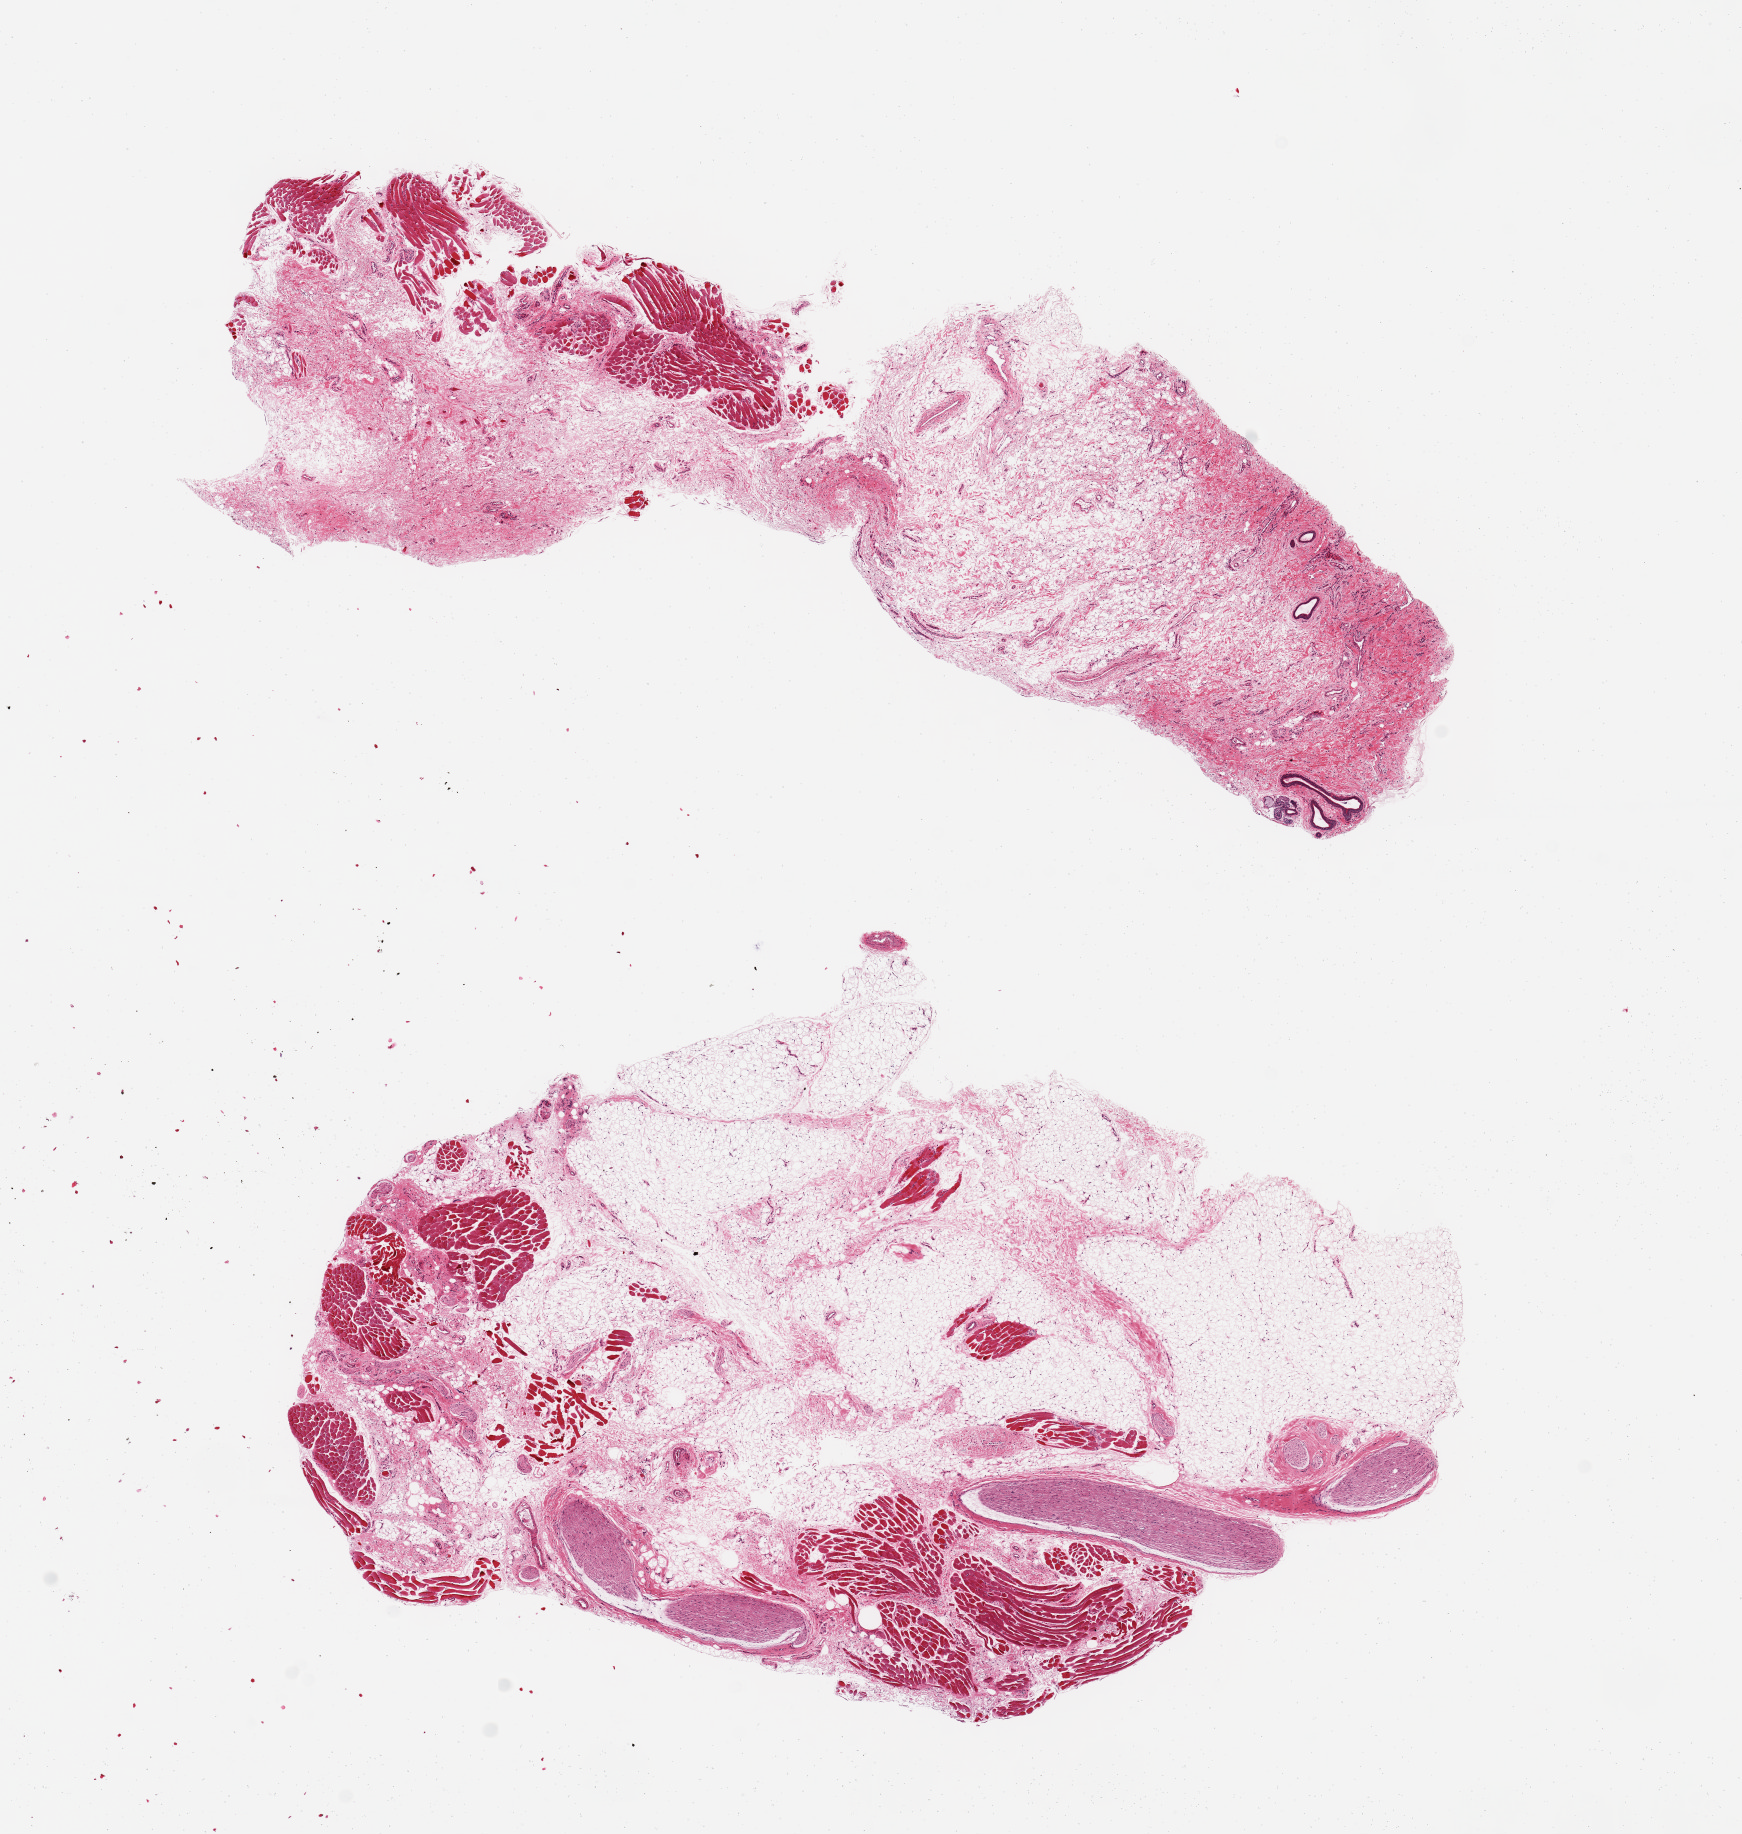
Digitized H&E-stained section — a low-resolution overview of the entire scanned area, about 13.8 x 14.5 mm (acquisition: 20x scan). PAXgene-fixed, paraffin-embedded tissue. Target tissue: minor salivary gland. Tissue donor sample. Donor sex: male.
• pathologist's review note for this sample: 2 pieces, 9x6 & 10x3.5mm; Virtually no salivary glands, except for 1x0.4mm focus. All skeletal muscle, nerve & fibroadipose tissue